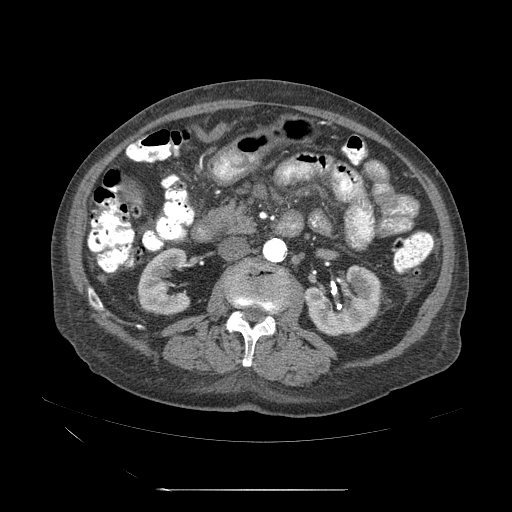
Contrast-enhanced abdominal CT (liver protocol), one axial slice. Slice 6 of 71 in the series (ordered by position). Reconstruction kernel STANDARD. 120 kVp. Soft-tissue window (W 400 / L 40 HU). 2.5 mm slice thickness. 512 × 512 image matrix. Case-level facts recorded for this patient, not image findings: diagnosis: hepatocellular carcinoma (patient treated with transarterial chemoembolisation; whether this scan precedes or follows treatment is not stated here); TNM stage (as recorded): Stage-II; Child-Pugh class: A; tumour nodularity: multinodular.
Annotated regions visible in this slice (semi-automatically segmented with operator editing):
- abdominal aorta: bounding box [x1, y1, x2, y2] px = [264, 238, 286, 264]